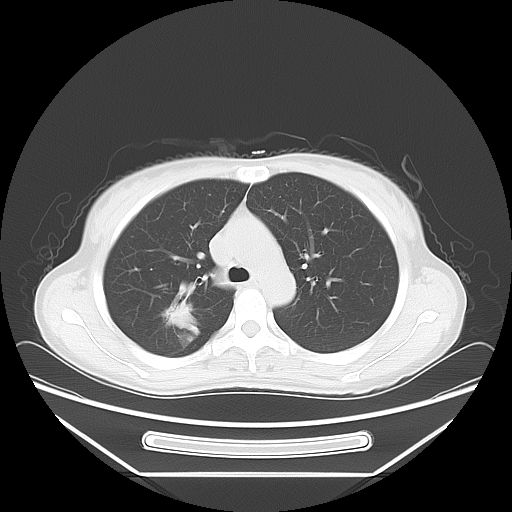
Chest CT, one axial slice. Slice 47 of 66 in the series (ordered by position). Lung window (W 1500 / L -600 HU). 512 × 512 image matrix. Female patient, age 37 years. From the clinical record (not read from this slice): clinical TNM (as recorded): T1c N0 M1.
Outlined on this slice (rectangle marked by the reading radiologist):
- lung tumour (recorded histology: adenocarcinoma): bounding box <157,297,203,339> (left, top, right, bottom; pixels)